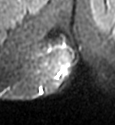
MRI of an extremity soft-tissue mass, one axial slice. Slice 11 of 49 in the series (ordered by position). STIR. MR volume resampled by the dataset authors to the PET/CT grid (not the native acquisition matrix). 115 × 125 image matrix, field of view 112 × 122 mm. Female patient. Case-level facts recorded for this patient, not image findings: histological type: epithelioid sarcoma; grade: intermediate; site of the primary tumour: right buttock.
Structures marked on this image (expert contour drawn on MRI and transferred to this co-registered scan by the dataset authors):
- gross tumour volume including surrounding oedema: bounding box (x1, y1, x2, y2) in pixels: (38, 48, 68, 88)